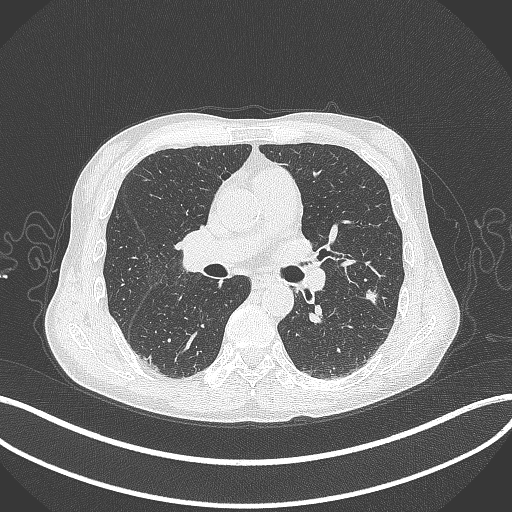
Chest CT, one axial slice; position 200 of 429 along the scan axis; lung window (W 1500 / L -600 HU); 512 × 512 image matrix. Patient: male, 58 years. From the clinical record (not read from this slice): clinical TNM (as recorded): T1c N0 M0; histopathological grade: G2.
Annotated regions visible in this slice (rectangle marked by the reading radiologist):
- lung tumour (recorded histology: adenocarcinoma): bounding box [x1, y1, x2, y2] px = [362, 284, 383, 311]